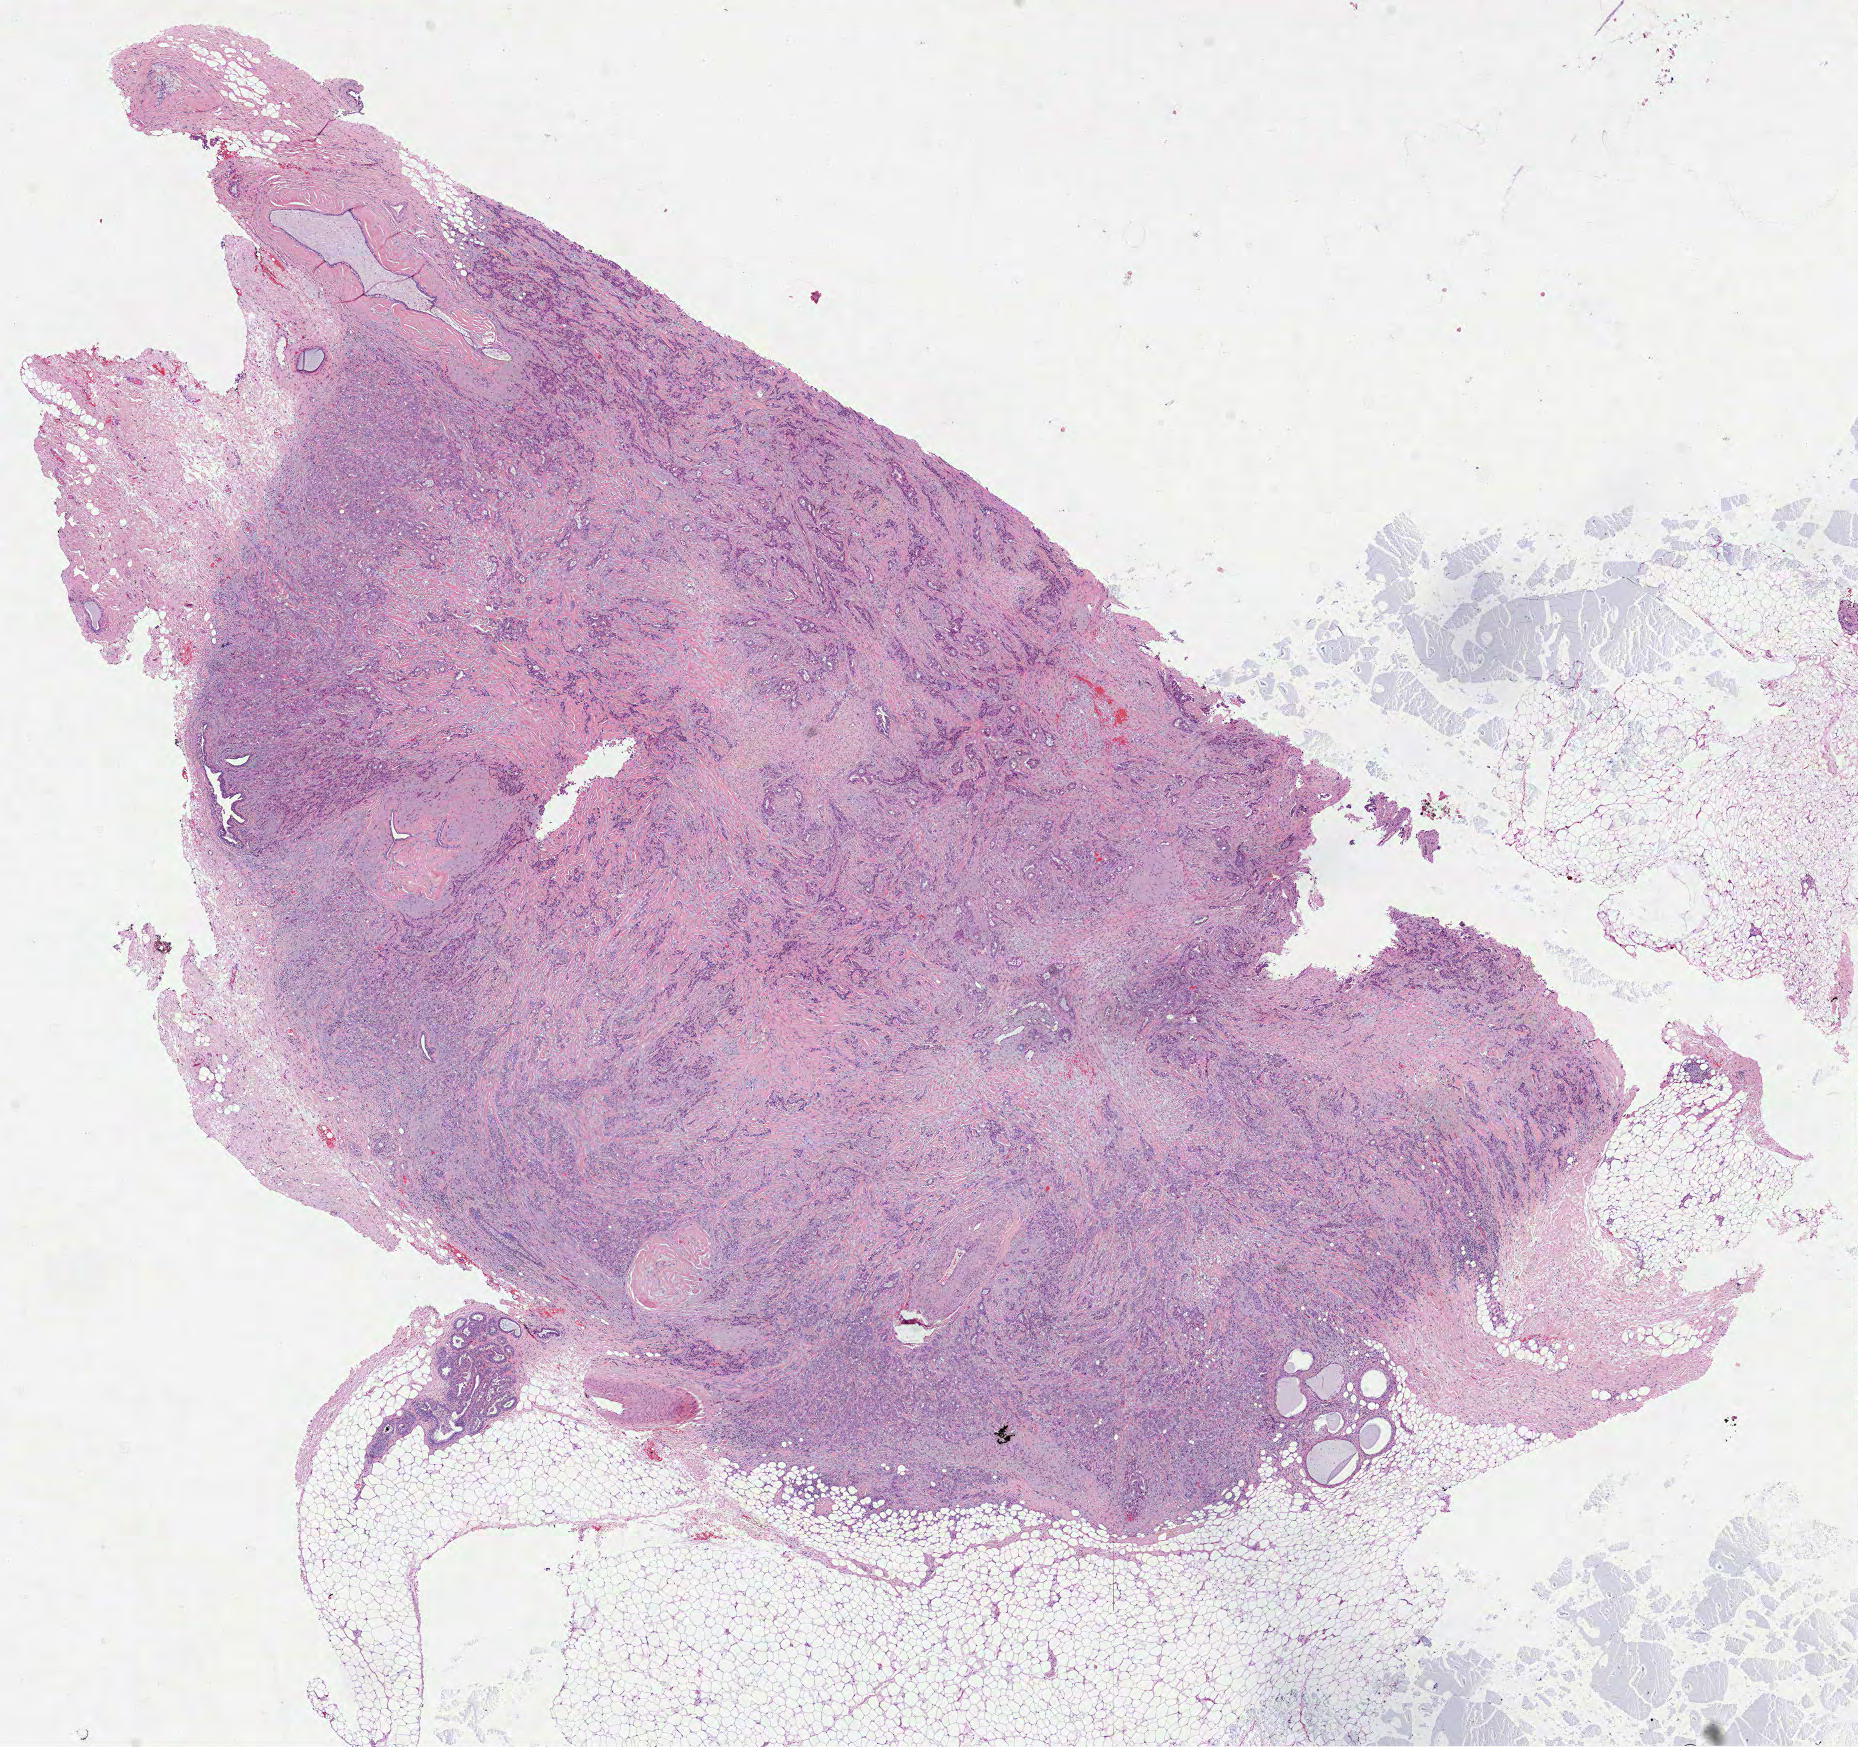
Whole-slide histology image, H&E-stained, a low-resolution overview of the entire scanned area, about 15.0 x 14.1 mm, formalin-fixed paraffin-embedded (FFPE) diagnostic section, sample: primary tumour, breast. Patient: female, age at initial diagnosis 76 years.
Lymph nodes positive (case pathology): 1 of 14 examined. Histologic diagnosis: Infiltrating duct carcinoma, NOS. AJCC pathologic stage: IIB (7th edition). TNM: T2 N1mi MX.